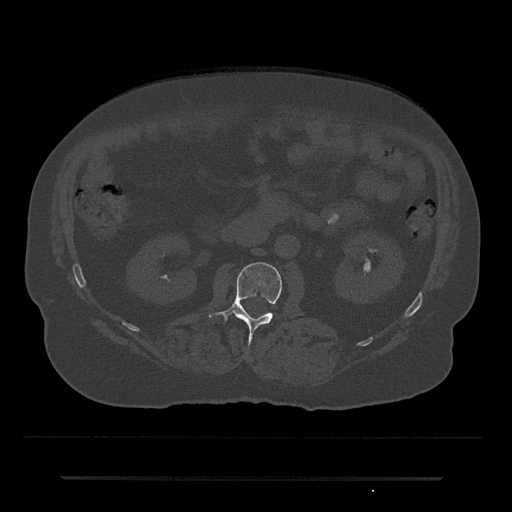
CT including the spine, one axial slice. Position 9 of 797 along the scan axis. 120 kVp. Bone window (W 1800 / L 400 HU). 512 × 512 image matrix. Male patient, age 69 years. Case-level facts recorded for this patient, not image findings: primary cancer: prostate.
Annotated regions visible in this slice (semi-automatic segmentation, software-assisted and operator-edited):
- L2 vertebra: box from (x=208, y=262) to (x=282, y=343) px